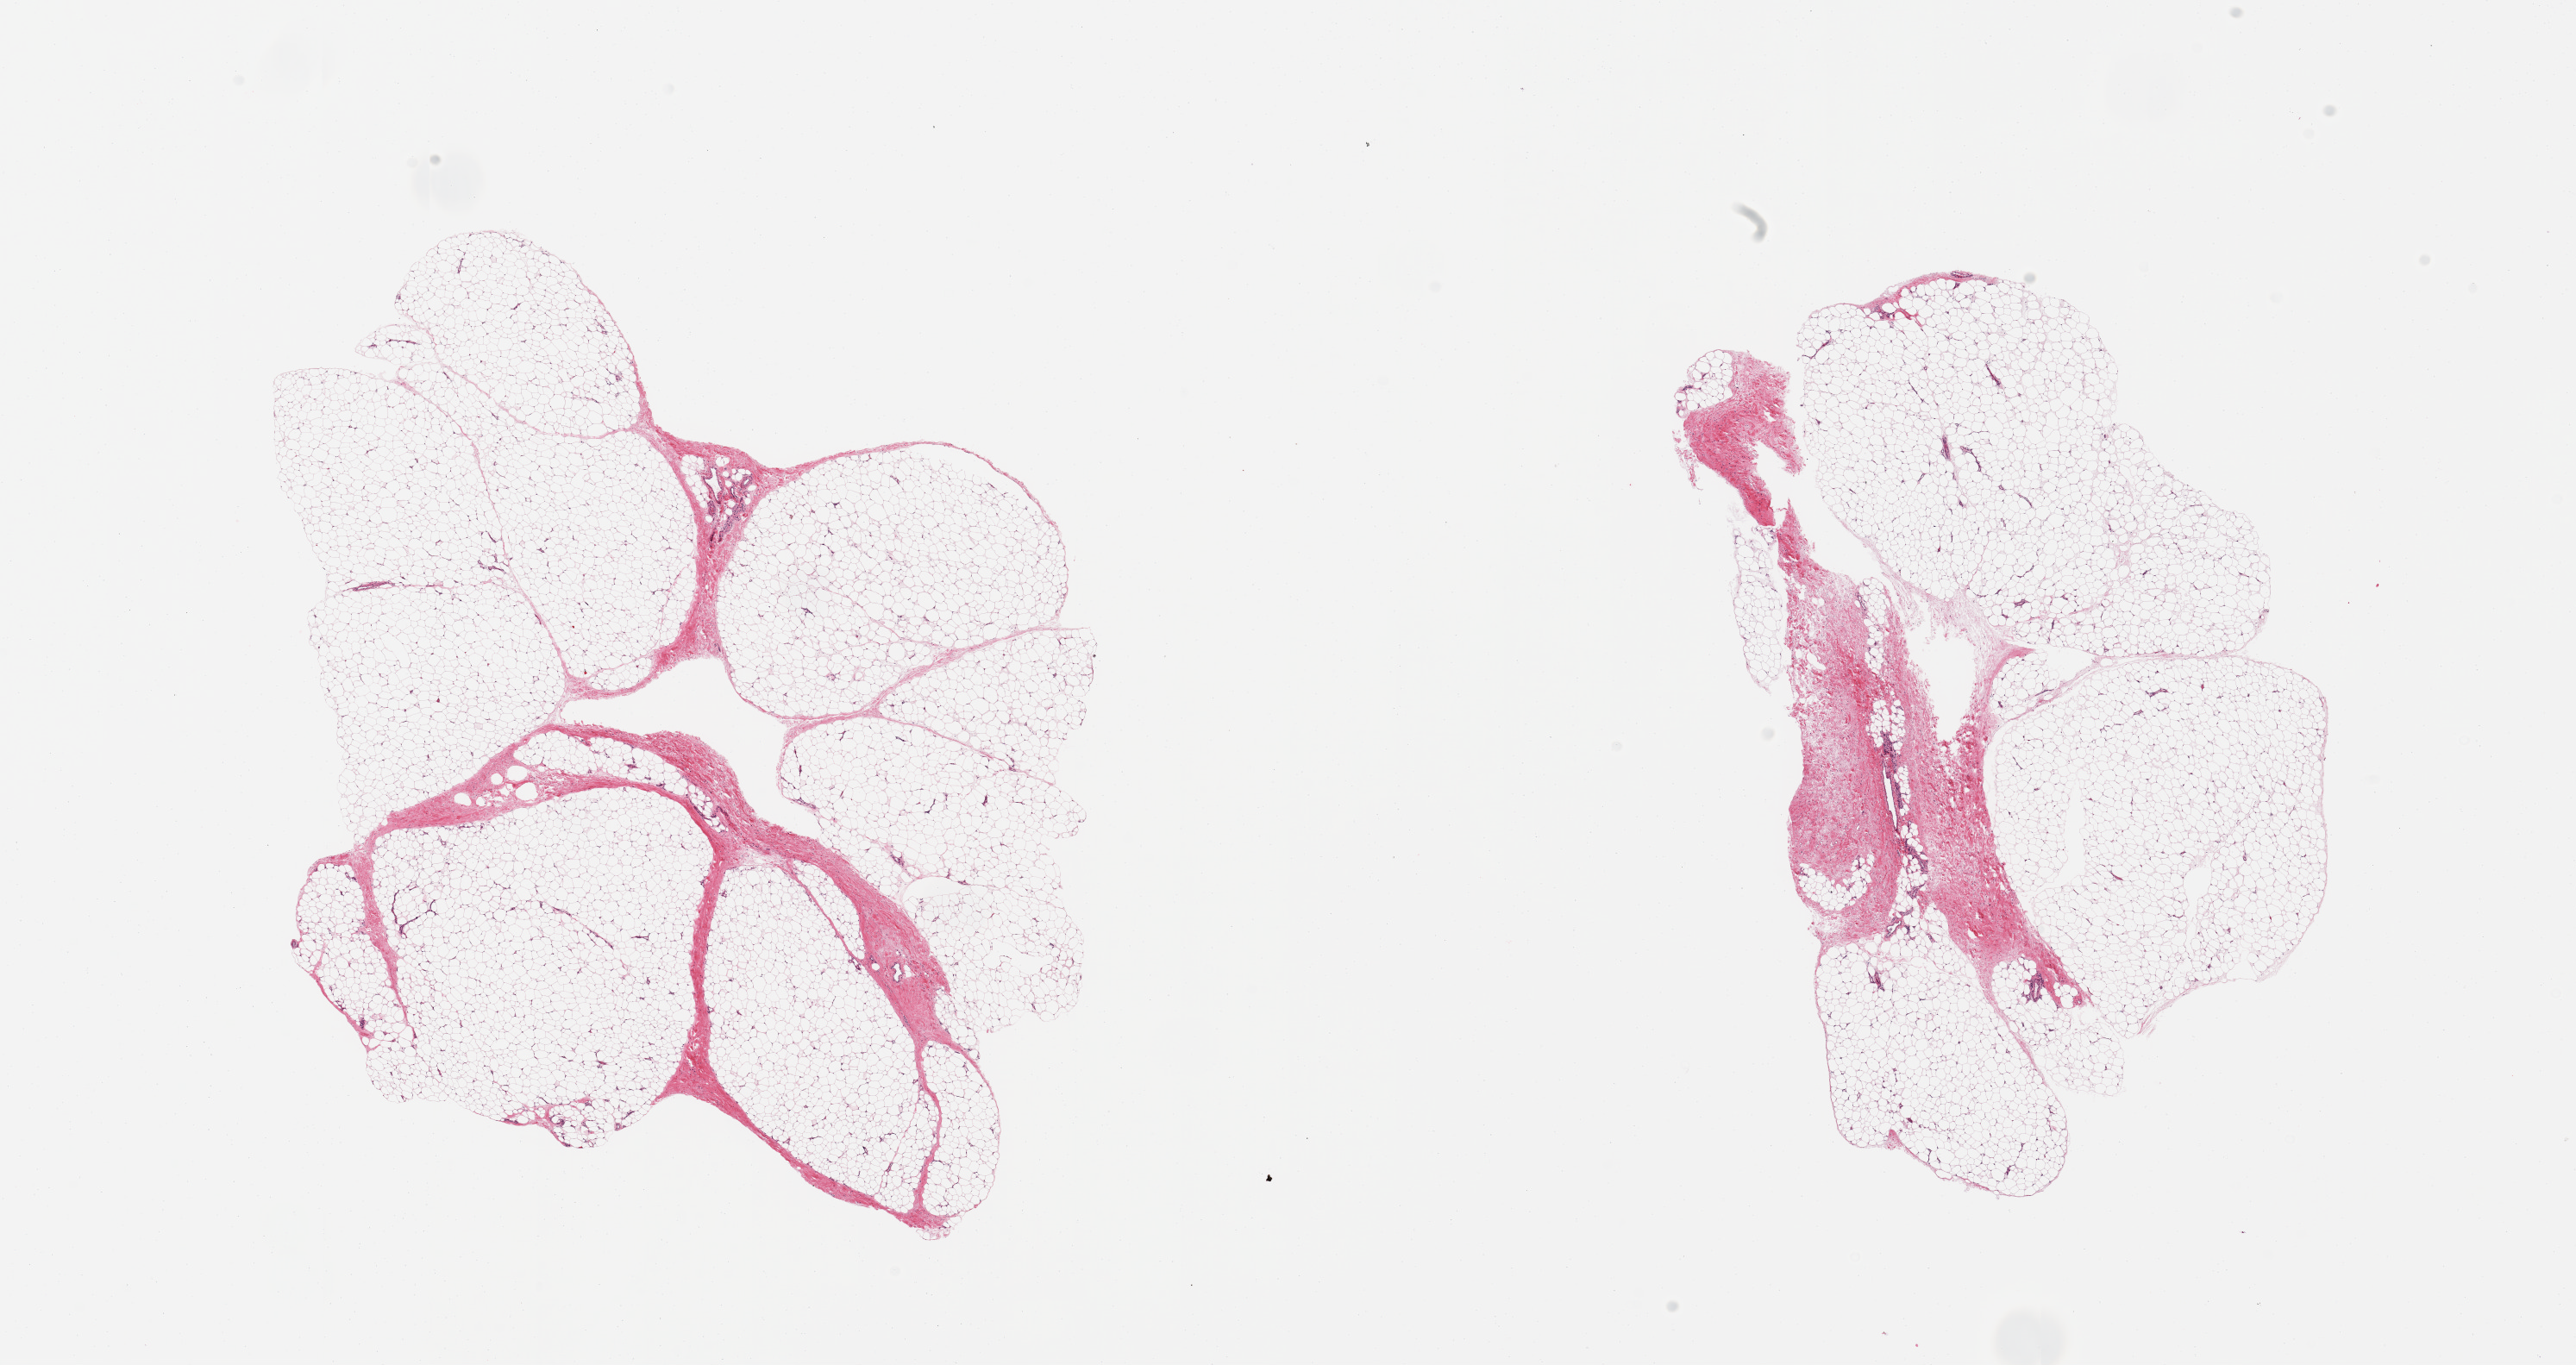
Digitized haematoxylin and eosin-stained section — low-resolution overview of the scanned area, about 23.6 x 12.5 mm (from a 20x scan). PAXgene-fixed paraffin-embedded (PFPE) section. Sampled site (target tissue): adipose tissue. Tissue donor sample.
• reviewer comment on this tissue sample: 2 pieces; 5 & 10% fibrous content